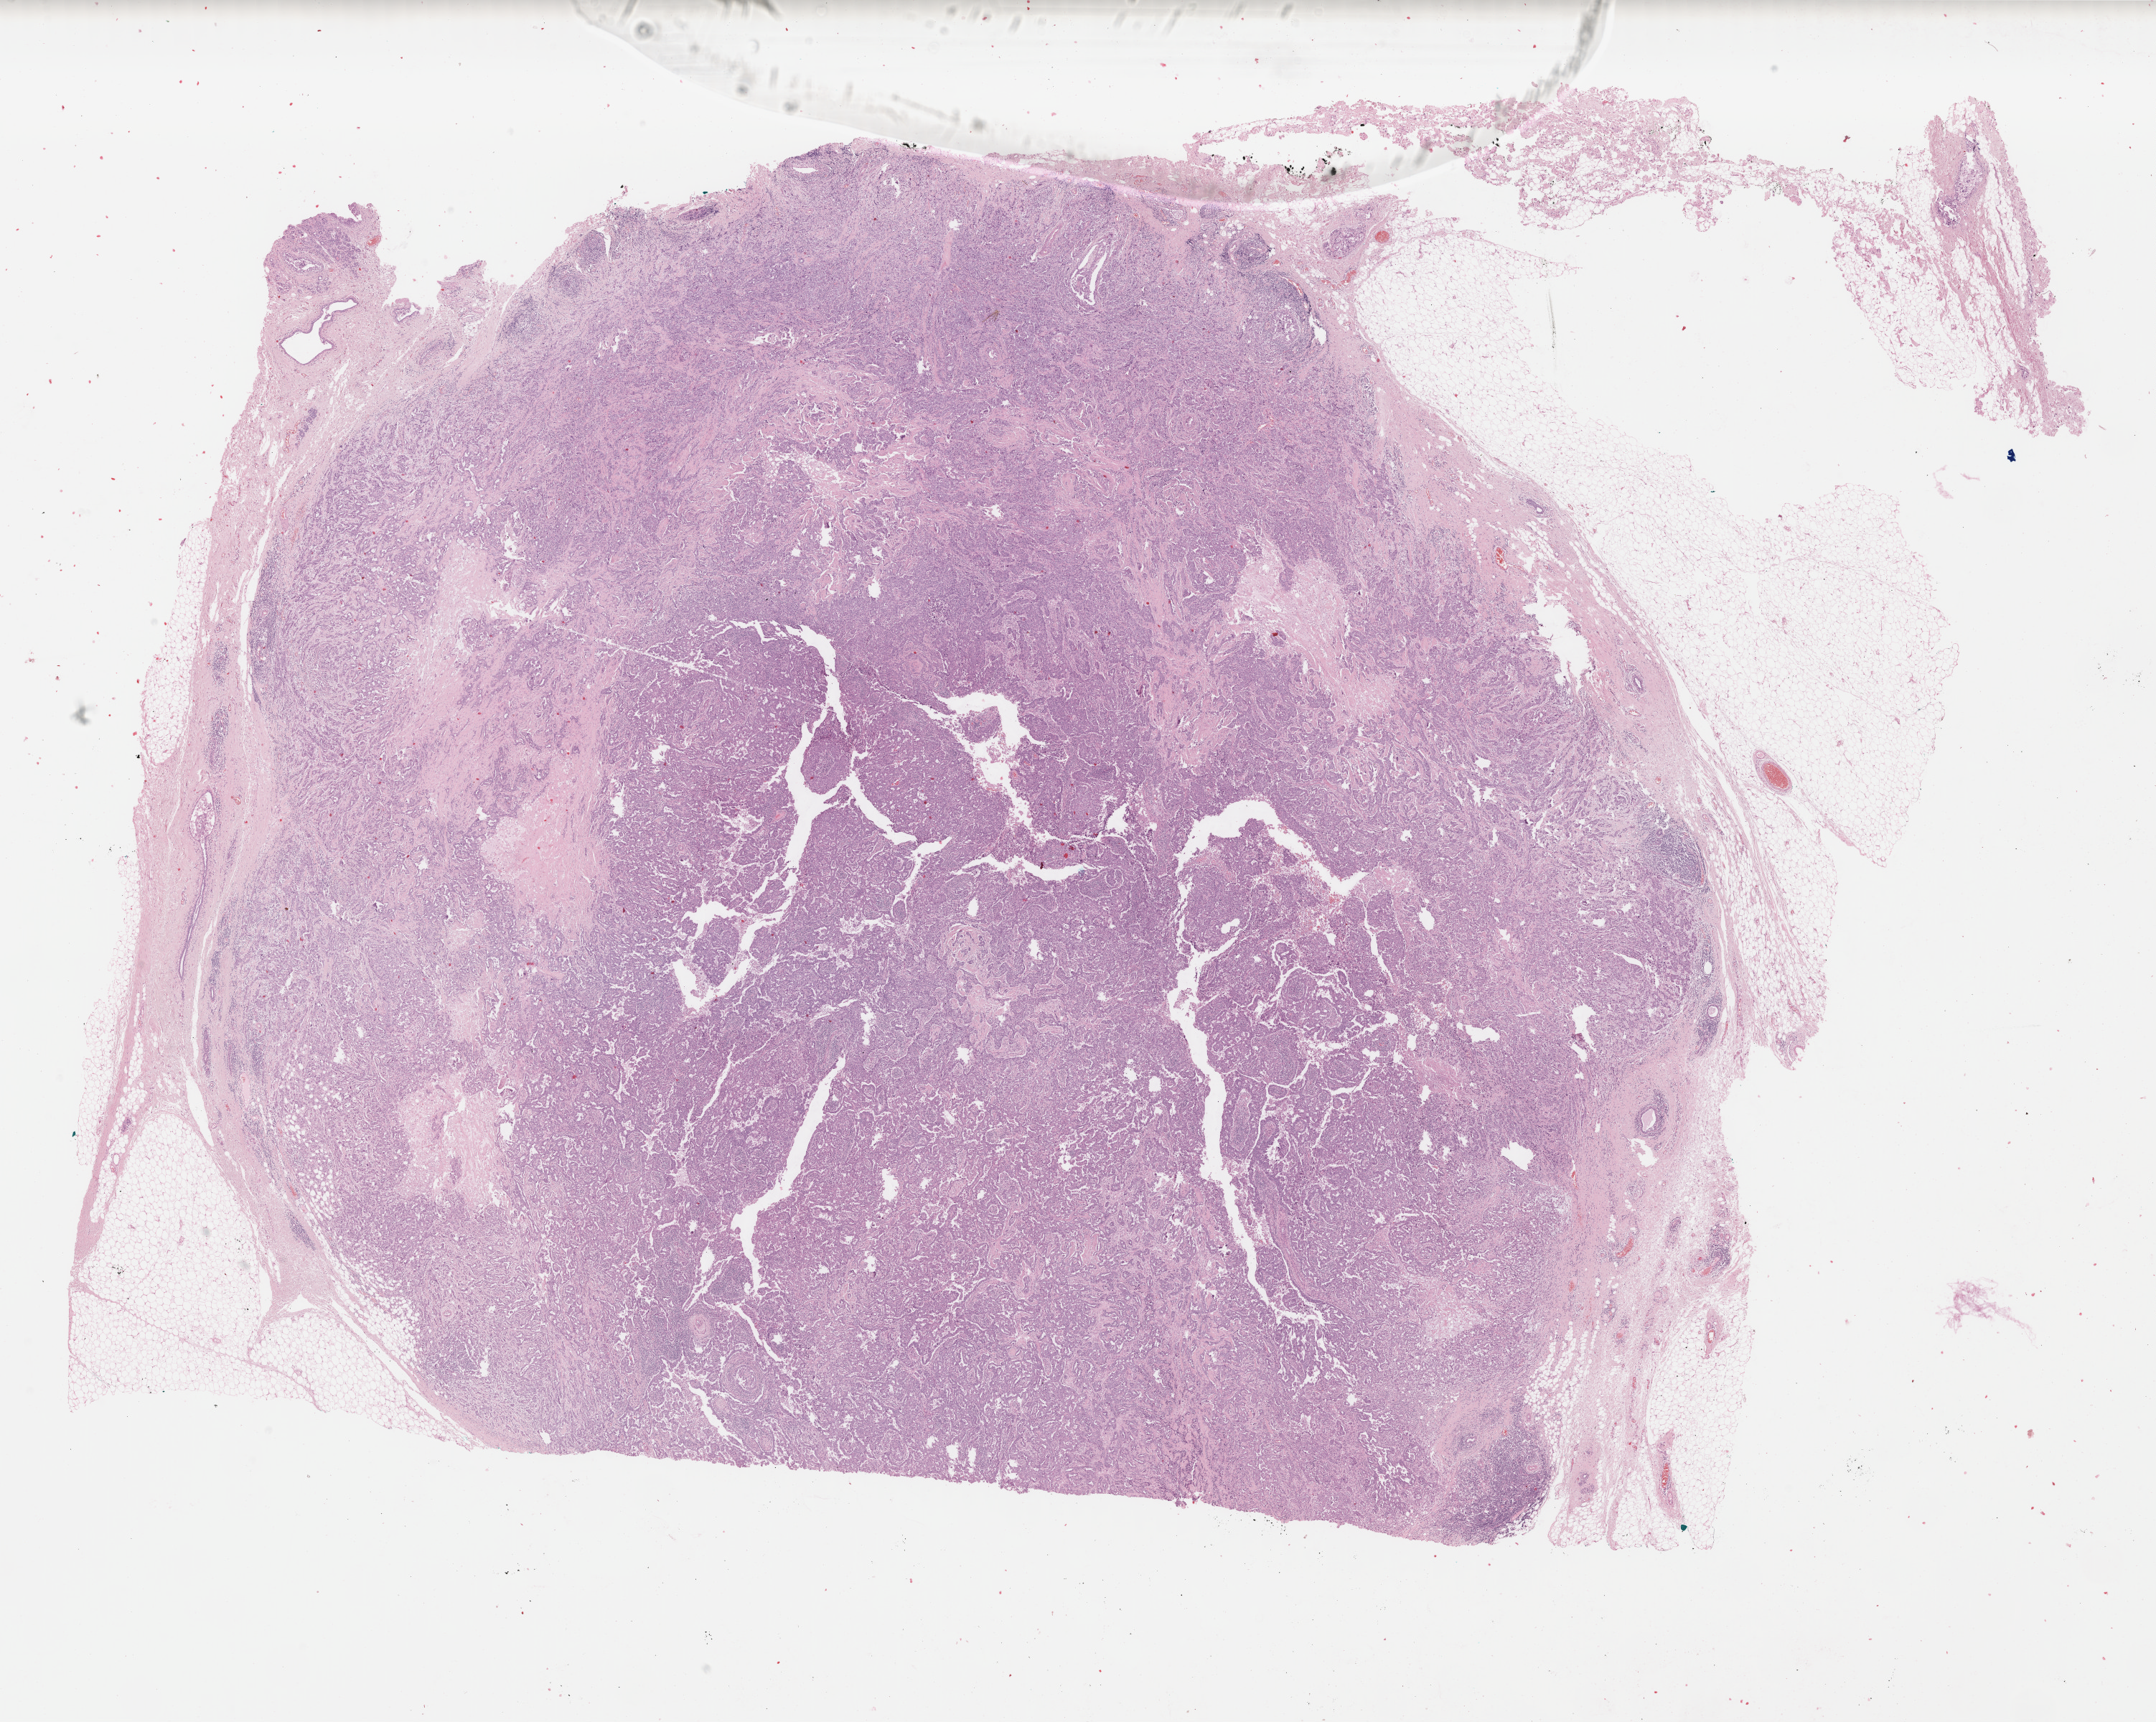
H&E-stained whole-slide image — a low-resolution overview of the entire scanned area, about 23.8 x 19.0 mm. Formalin-fixed paraffin-embedded (FFPE) diagnostic section. Sample: primary tumour, breast. Female patient; age at initial diagnosis 77 years.
Histologic diagnosis: Infiltrating duct carcinoma, NOS.